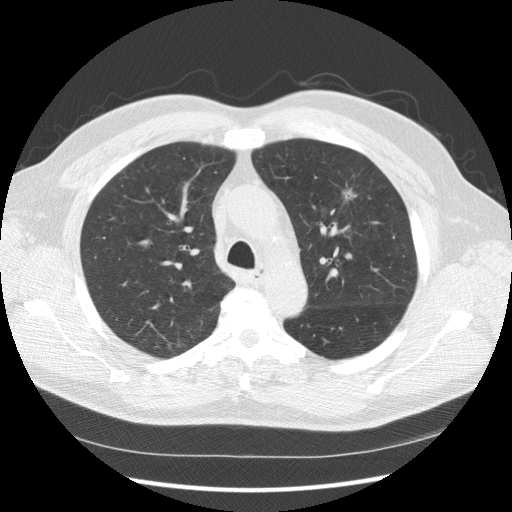
Low-dose screening chest CT, axial slice, second screening round (one year after baseline), lung window (W 1500 / L -600 HU), slice 47 of 157 in the series. Male, age 65 years at enrolment. Current smoker at enrolment.
Lesion marked by an expert reader, bounding box <327,175,372,220> (left, top, right, bottom; pixels). The screening reader recorded 2 non-calcified nodules or masses ≥4 mm on this exam (left upper lobe, right upper lobe); which of them this box marks is not recorded. Official screen result: positive, other. Later outcome: lung cancer diagnosed 120 days after this screen — carcinoma, NOS, left upper lobe, poorly differentiated (G3), stage IIIA (AJCC 6th edition), 25 mm at pathology.